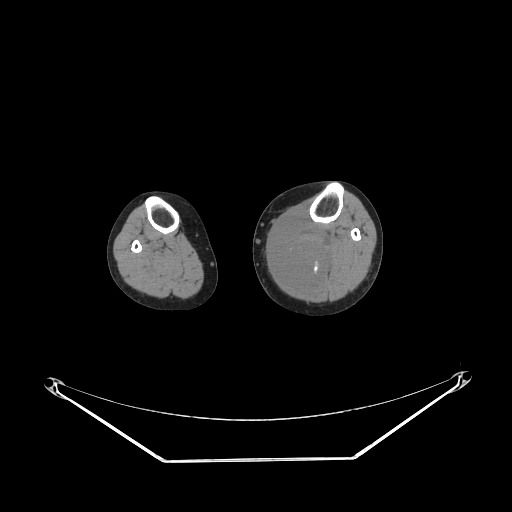
CT of an extremity soft-tissue mass (from a PET/CT study), one axial slice. Position 147 of 223 along the scan axis. Soft-tissue window (W 400 / L 40 HU). 3.75 mm slice thickness. 512 × 512 image matrix, field of view 500 × 500 mm. Female patient. From the clinical record (not read from this slice): histological type: extraskeletal high grade osteogenic sarcoma; grade: high; site of the primary tumour: left calf.
Outlined on this slice (expert contour drawn on MRI and transferred to this co-registered scan by the dataset authors):
- gross tumour volume (mass): bounding box [x1, y1, x2, y2] px = [270, 219, 332, 284]